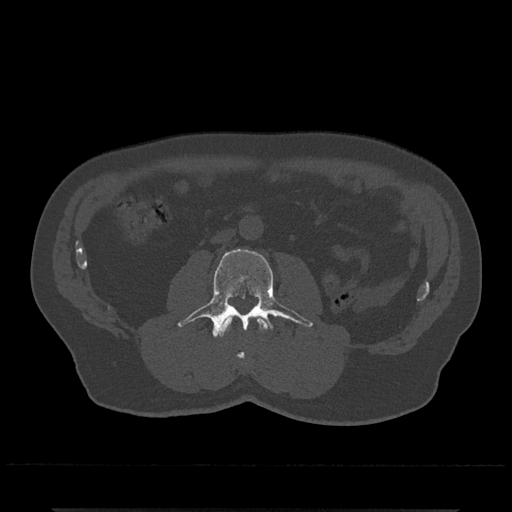
CT including the spine, one axial slice; slice 232 of 797 in the series (ordered by position); reconstruction kernel Br40s/3; 120 kVp; bone window (W 1800 / L 400 HU); 0.5 mm slice thickness; 512 × 512 image matrix. Patient: male, 67 years. Case-level facts recorded for this patient, not image findings: primary cancer: prostate.
Annotated regions visible in this slice (semi-automatic segmentation, software-assisted and operator-edited):
- L2 vertebra: box from (x=218, y=316) to (x=269, y=360) px
- L3 vertebra: (x=177, y=249)–(x=313, y=337)